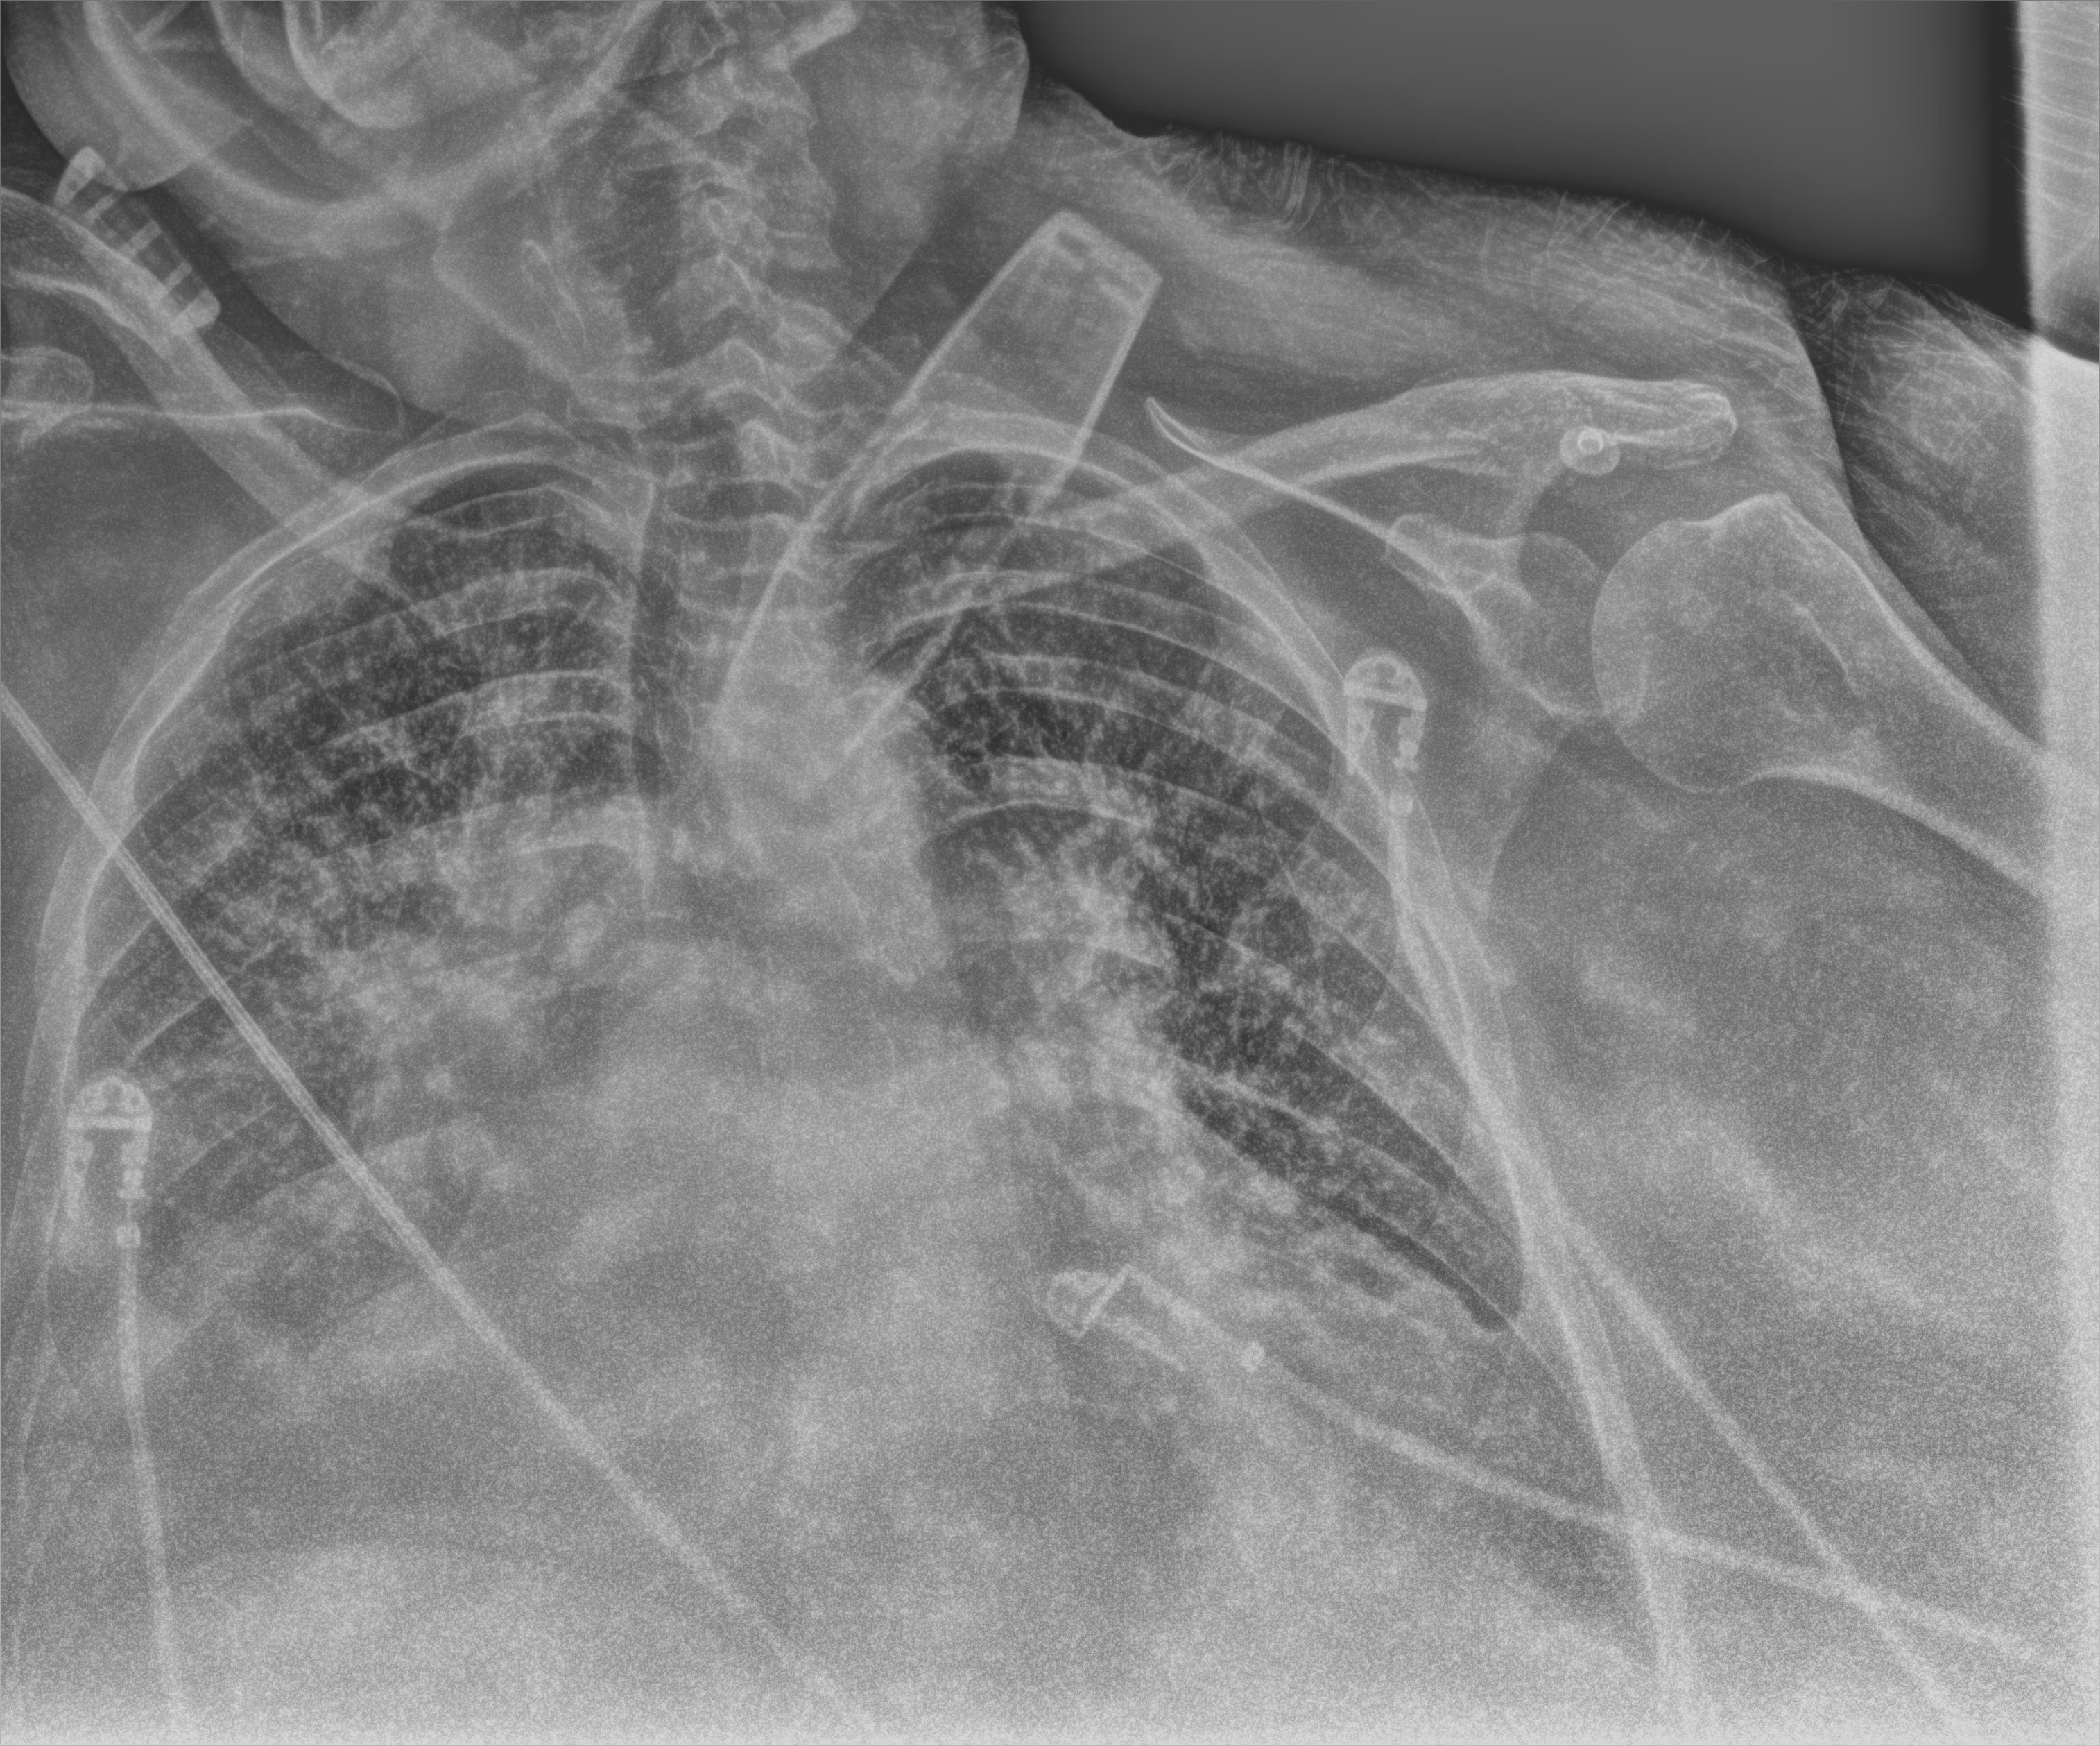
Portable chest radiograph. Patient hospitalised with COVID-19; female, aged 60–74 years.
Admission-level facts for this patient (not findings on this image; timing relative to this image not recorded): chronic kidney disease (admission record): no; mechanically ventilated during this hospital stay: yes; length of hospital stay: 6 days.